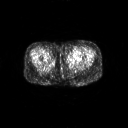
FDG PET of an extremity soft-tissue mass (from a PET/CT study), one axial slice; 3.27 mm slice thickness; 128 × 128 image matrix, field of view 700 × 700 mm. Patient: female, 47 years. Case-level facts recorded for this patient, not image findings: histological type: myxofibrosarcoma; grade: intermediate; site of the primary tumour: left thigh.
Annotated regions visible in this slice (expert contour drawn on MRI and transferred to this co-registered scan by the dataset authors):
- gross tumour volume including surrounding oedema: bounding box <67,54,82,62> (left, top, right, bottom; pixels)